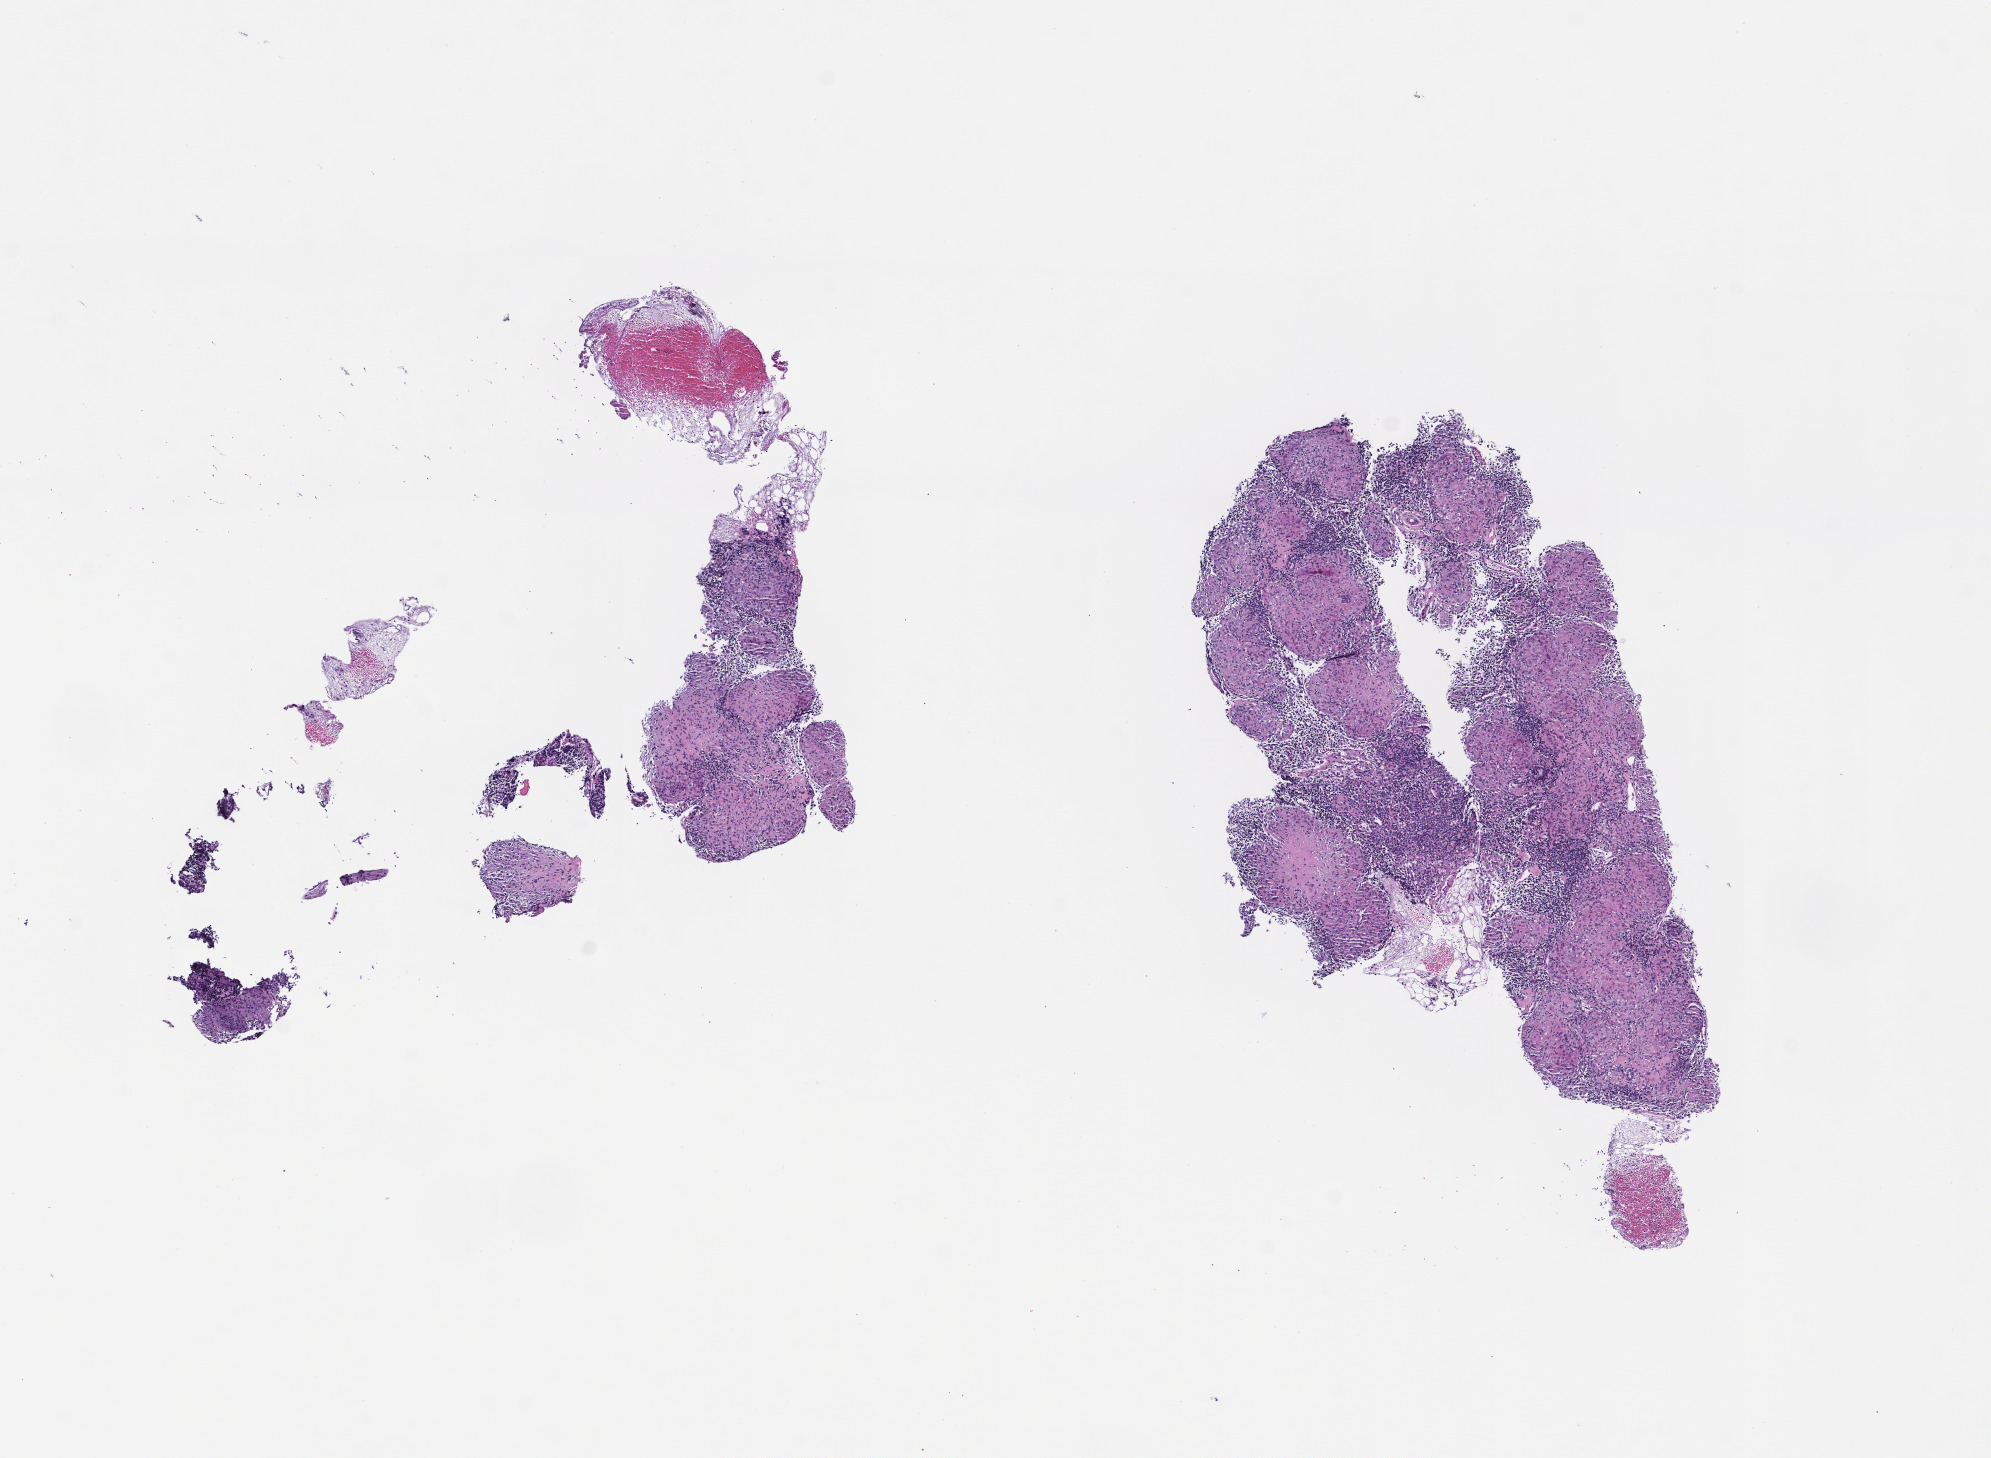
Haematoxylin and eosin whole-slide image — low-resolution overview of the scanned area, about 8.0 x 5.9 mm; formalin-fixed, paraffin-embedded (FFPE) tissue; specimen time point: collected at baseline (before treatment). Patient sex: male.
- this section: metastatic tumor tissue
- primary diagnosis of the patient: Non-Small Cell Lung Carcinoma